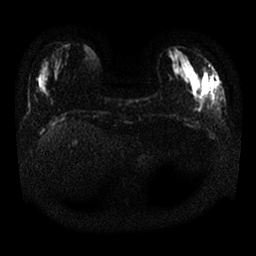
Breast MRI, one axial slice; slice 7 of 25 in the series (ordered by position); diffusion-weighted series; image 2 of 4 stored at this slice position (different b-values; order by instance number); 1.5 T; 4 mm slice thickness; 256 × 256 image matrix, field of view 340 × 340 mm. Female patient.
Structures marked on this image (expert manual segmentation):
- tumour on diffusion-weighted imaging: bounding box [x1, y1, x2, y2] px = [204, 72, 214, 94]